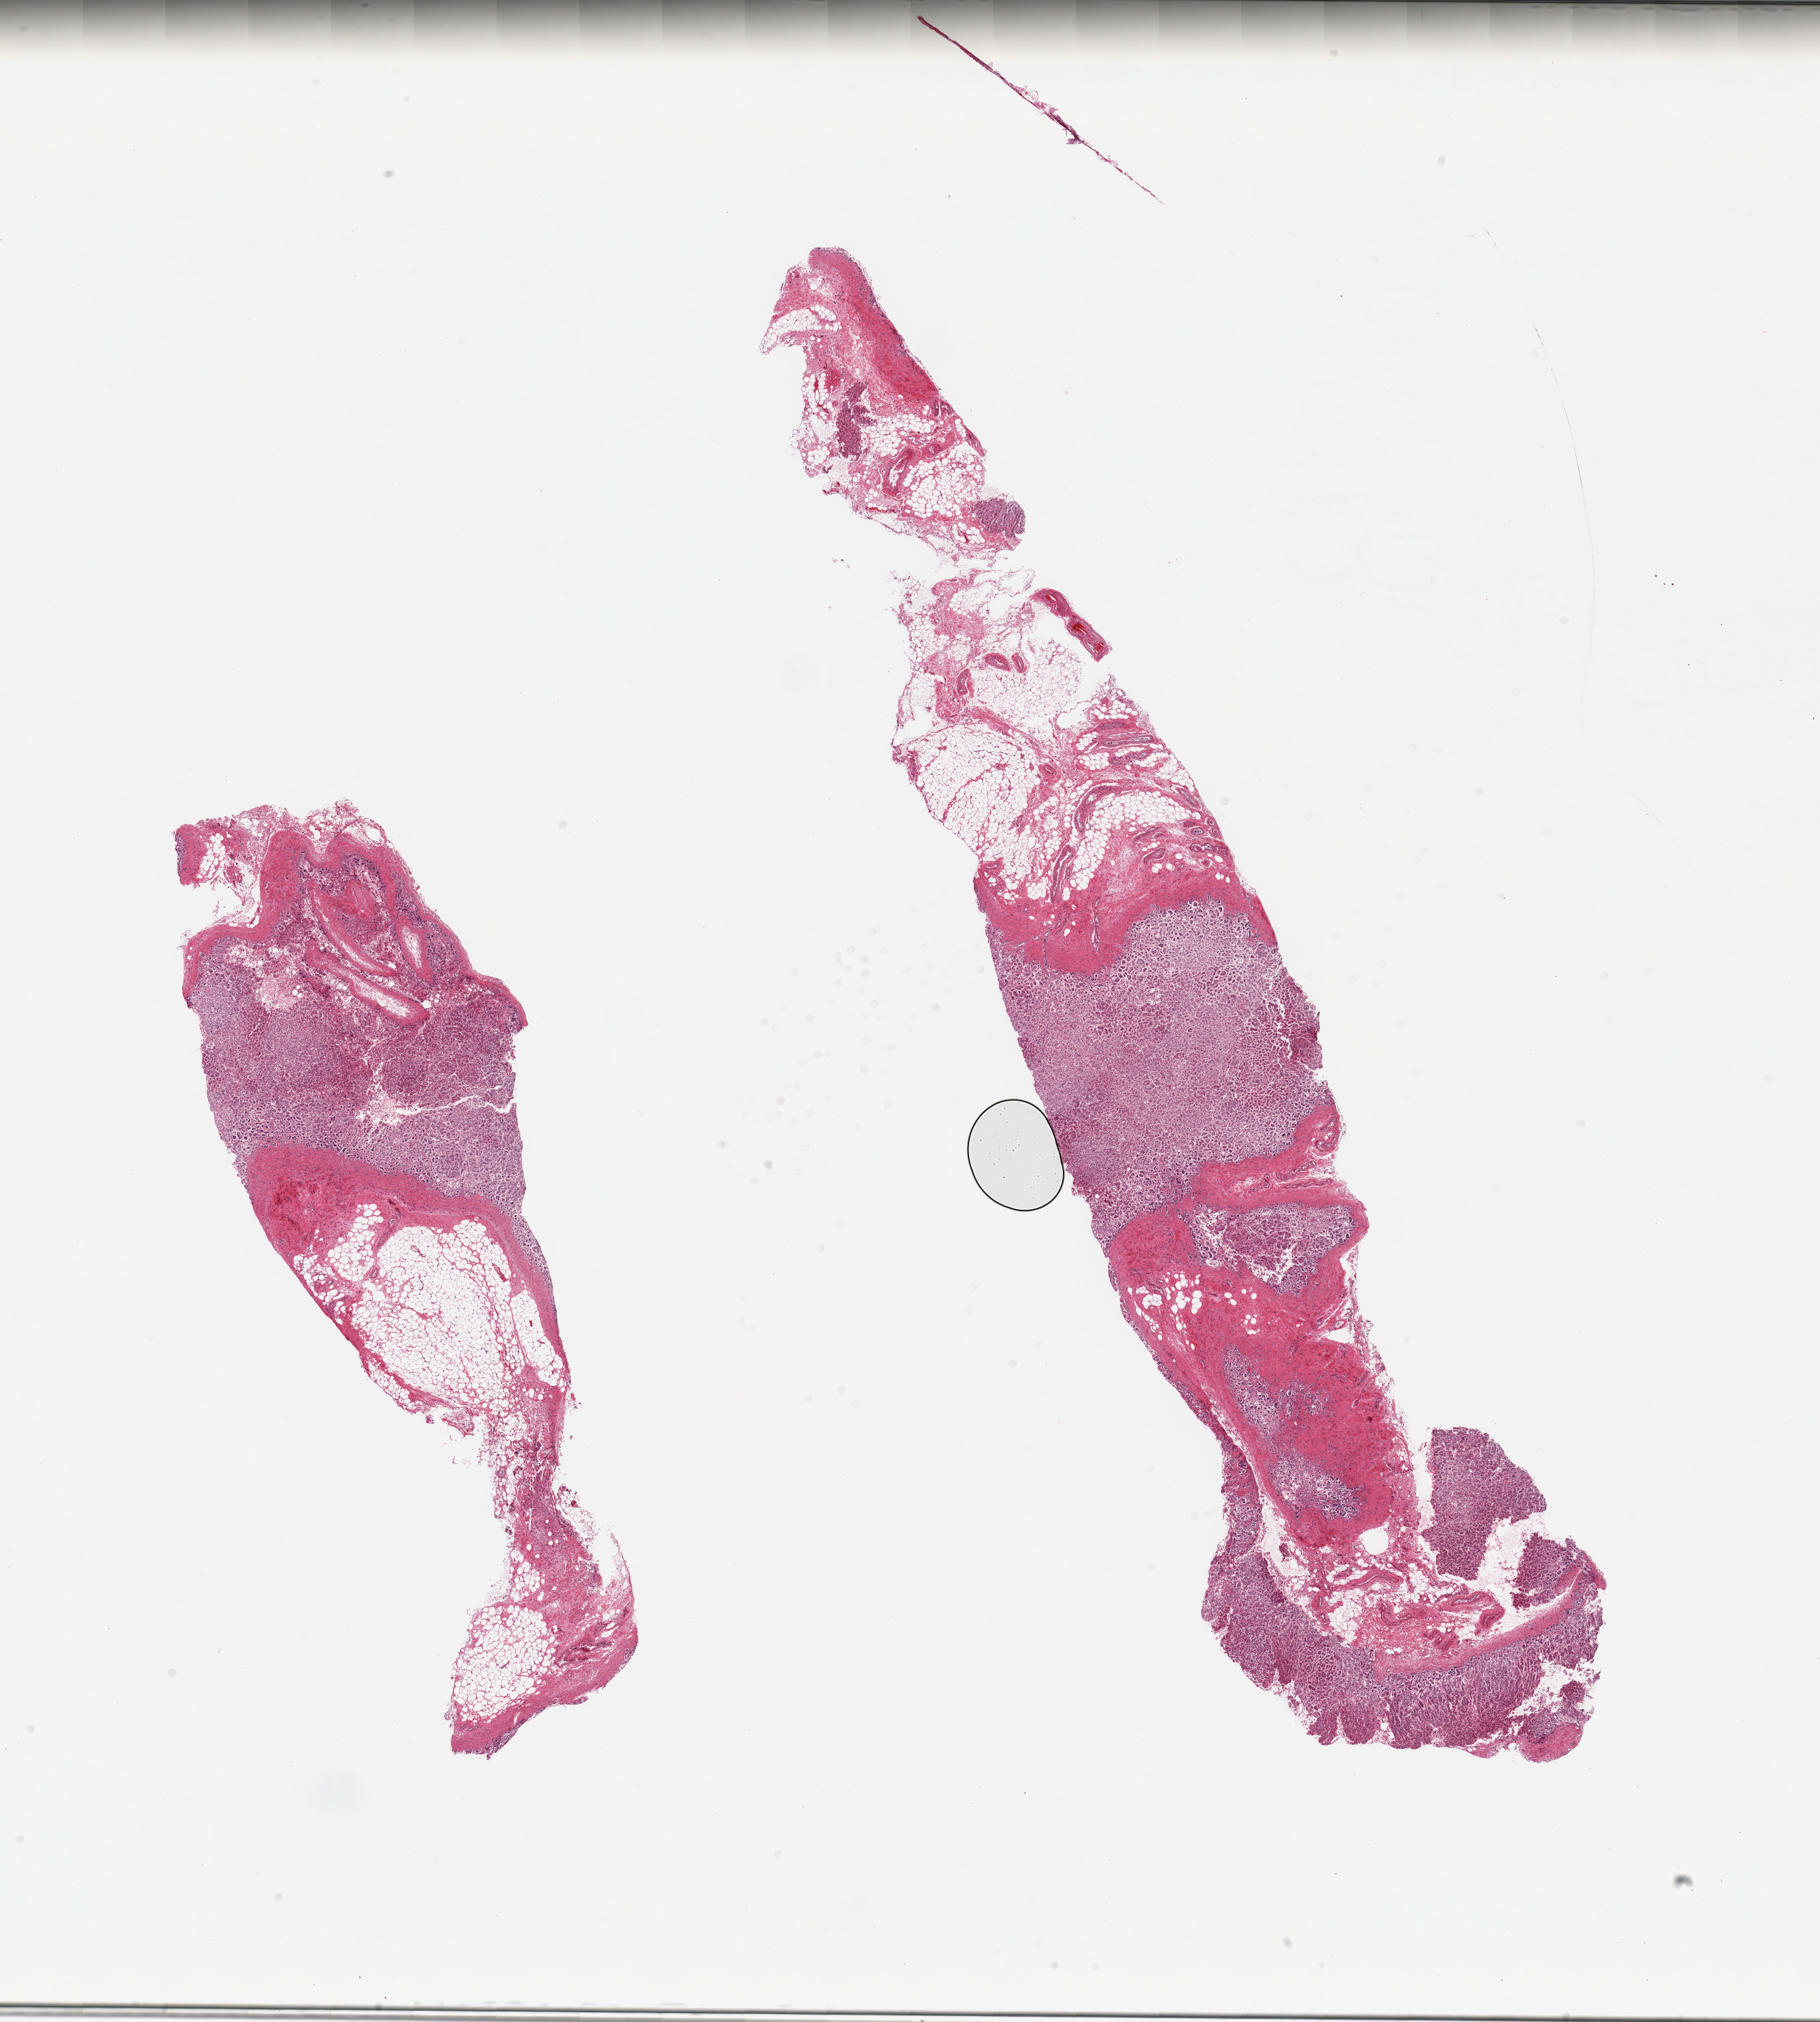
Hematoxylin and eosin (H&E) whole-slide image, brightfield, whole scanned area (about 21.7 x 24.1 mm) shown as a low-resolution overview; PAXgene-fixed paraffin-embedded (PFPE) section; sampled site (target tissue): adrenal gland; tissue donor sample. Donor: male.
• review note (as recorded): 2 pieces; ~50% external fat and autolyzed cortex grade 2/3